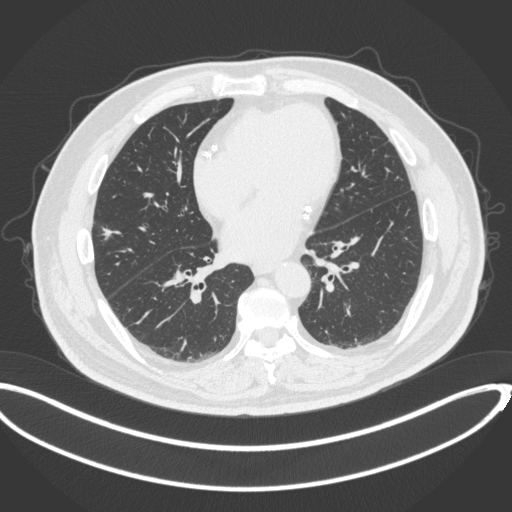
Chest CT, one axial slice. Position 137 of 342 along the scan axis. 120 kVp. Lung window (W 1500 / L -600 HU). 512 × 512 image matrix, field of view 427 × 427 mm. Patient: male, 68 years. Case-level facts recorded for this patient, not image findings: clinical TNM (as recorded): T1c N0 M0.
Structures marked on this image (rectangle marked by the reading radiologist):
- lung tumour (recorded histology: adenocarcinoma): box from (x=100, y=225) to (x=112, y=242) px